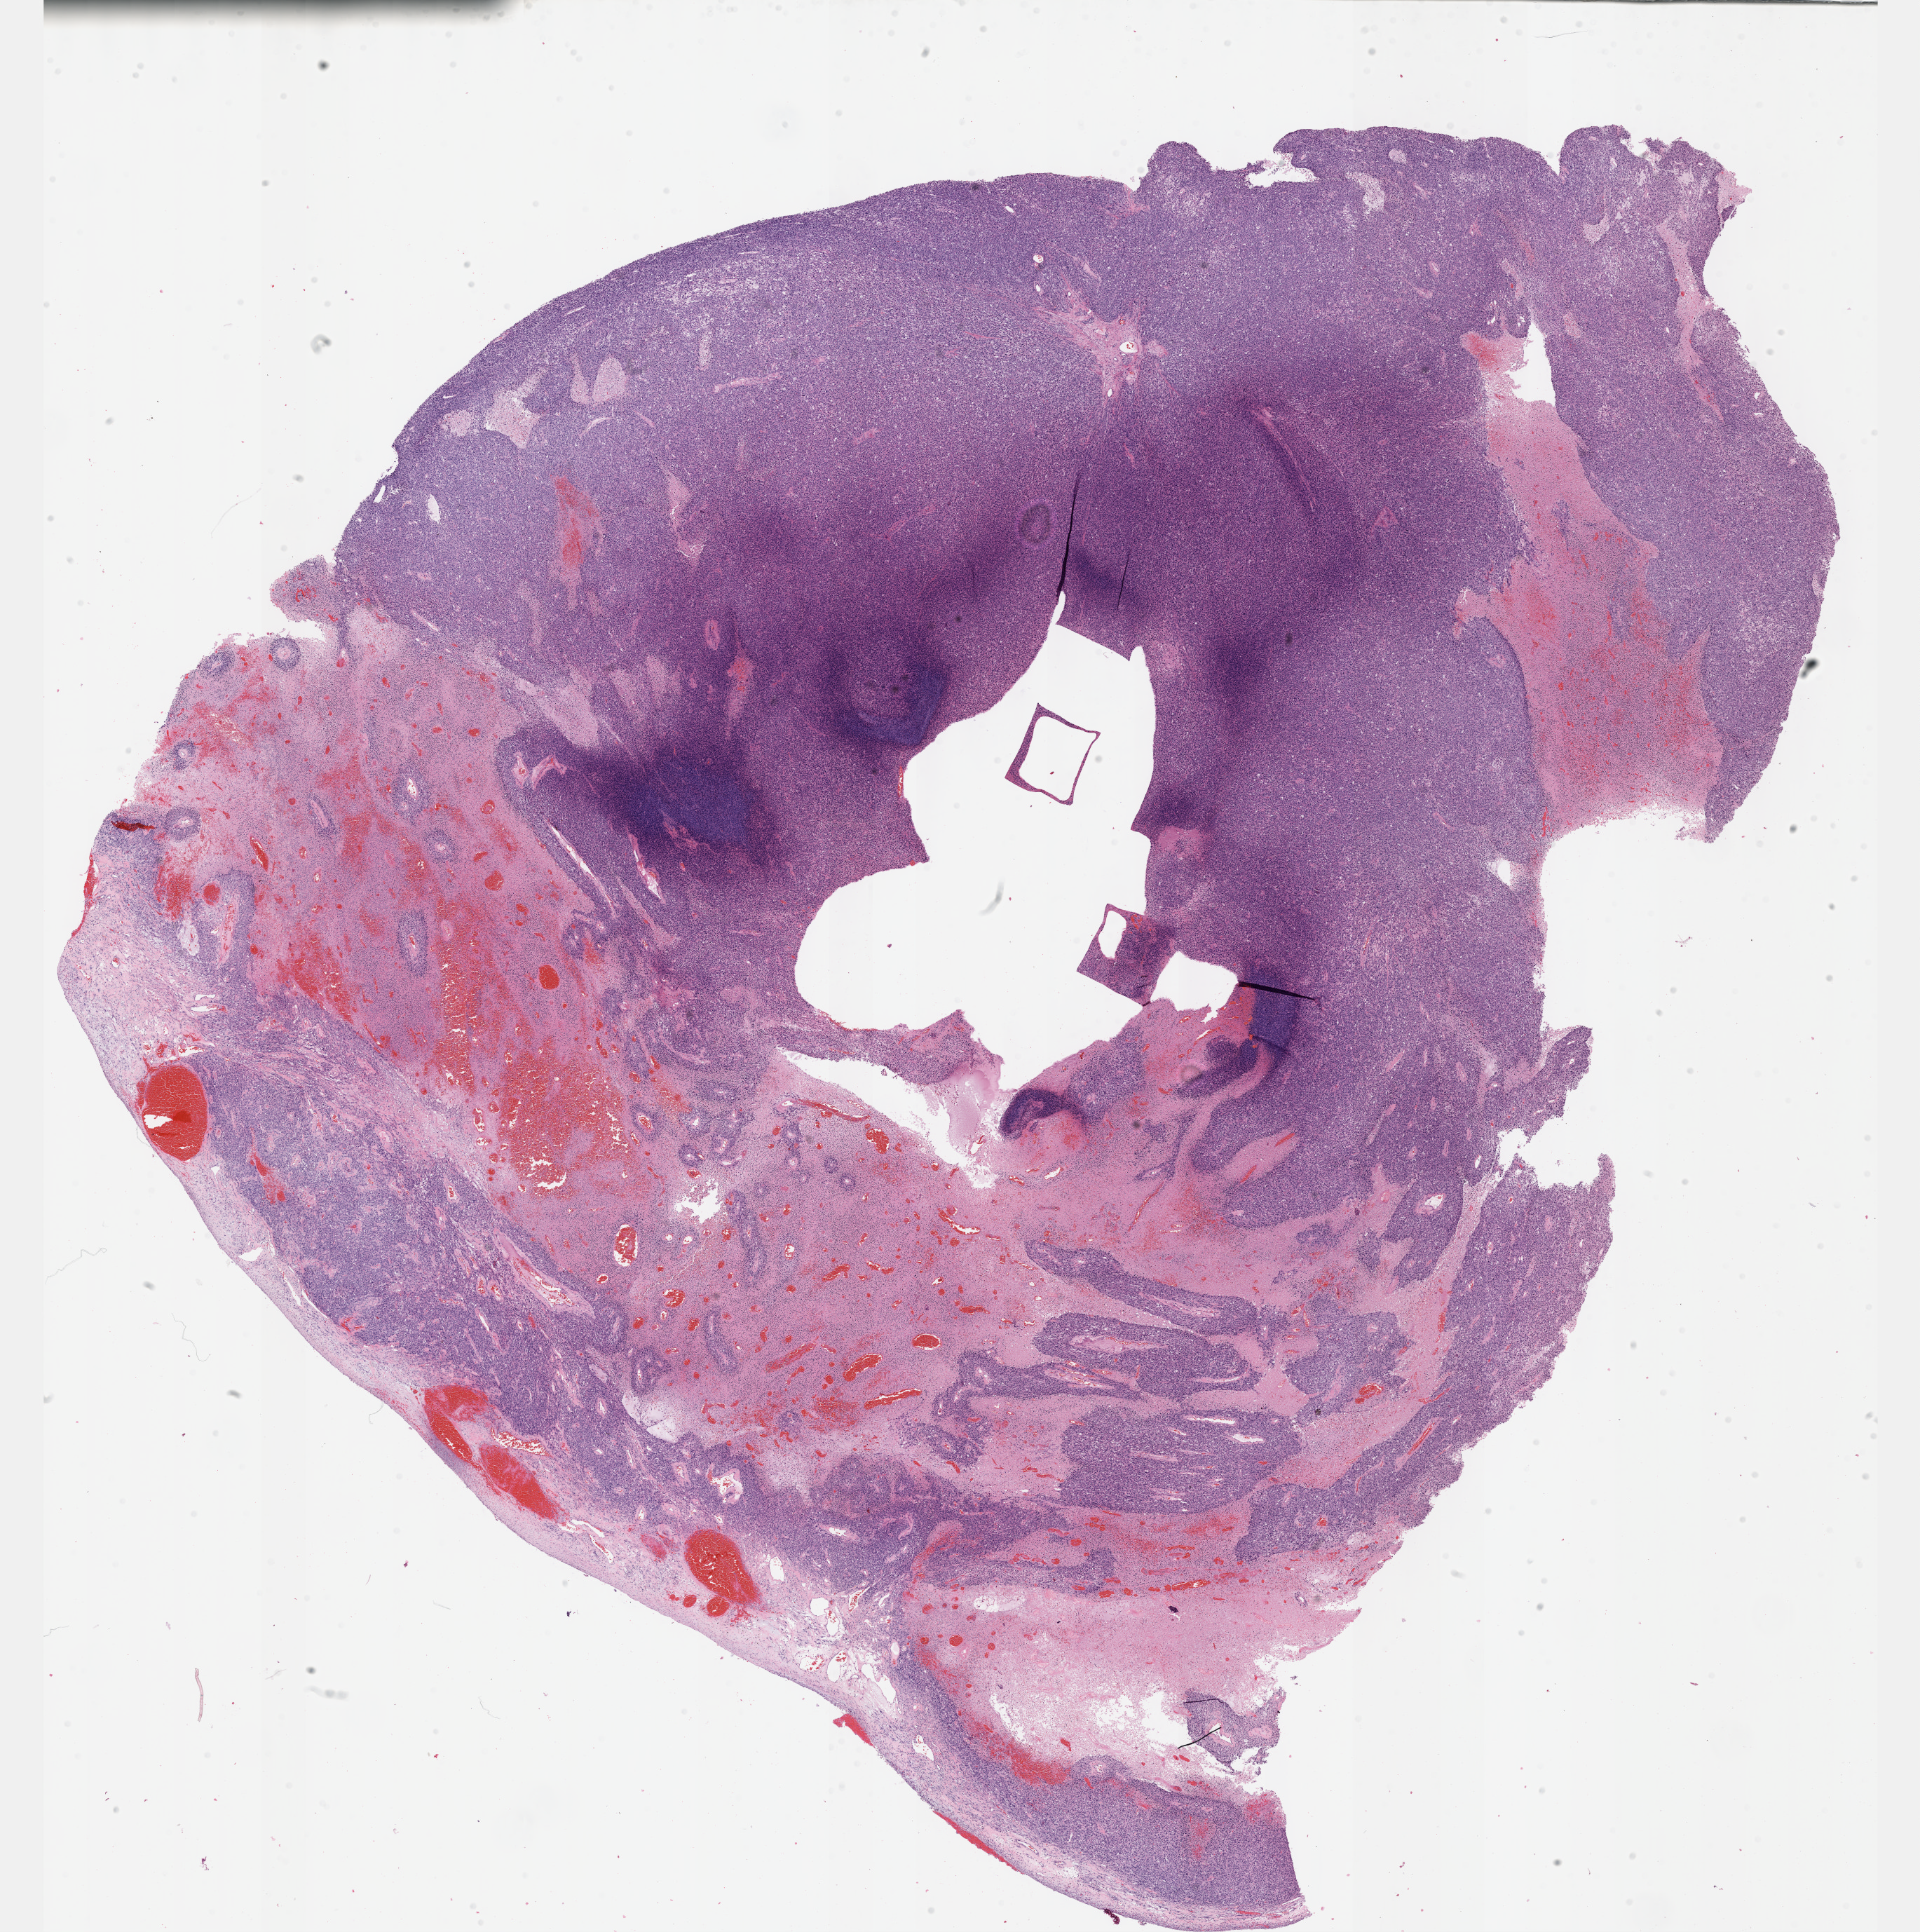
Digitized H&E-stained tissue section (whole slide), a low-resolution overview of the entire scanned area, about 22.1 x 22.3 mm, formalin-fixed paraffin-embedded (FFPE) diagnostic section, primary tumour sample from the uterus. Patient: female, age at initial diagnosis 58 years.
* pathologic diagnosis: Leiomyosarcoma, NOS